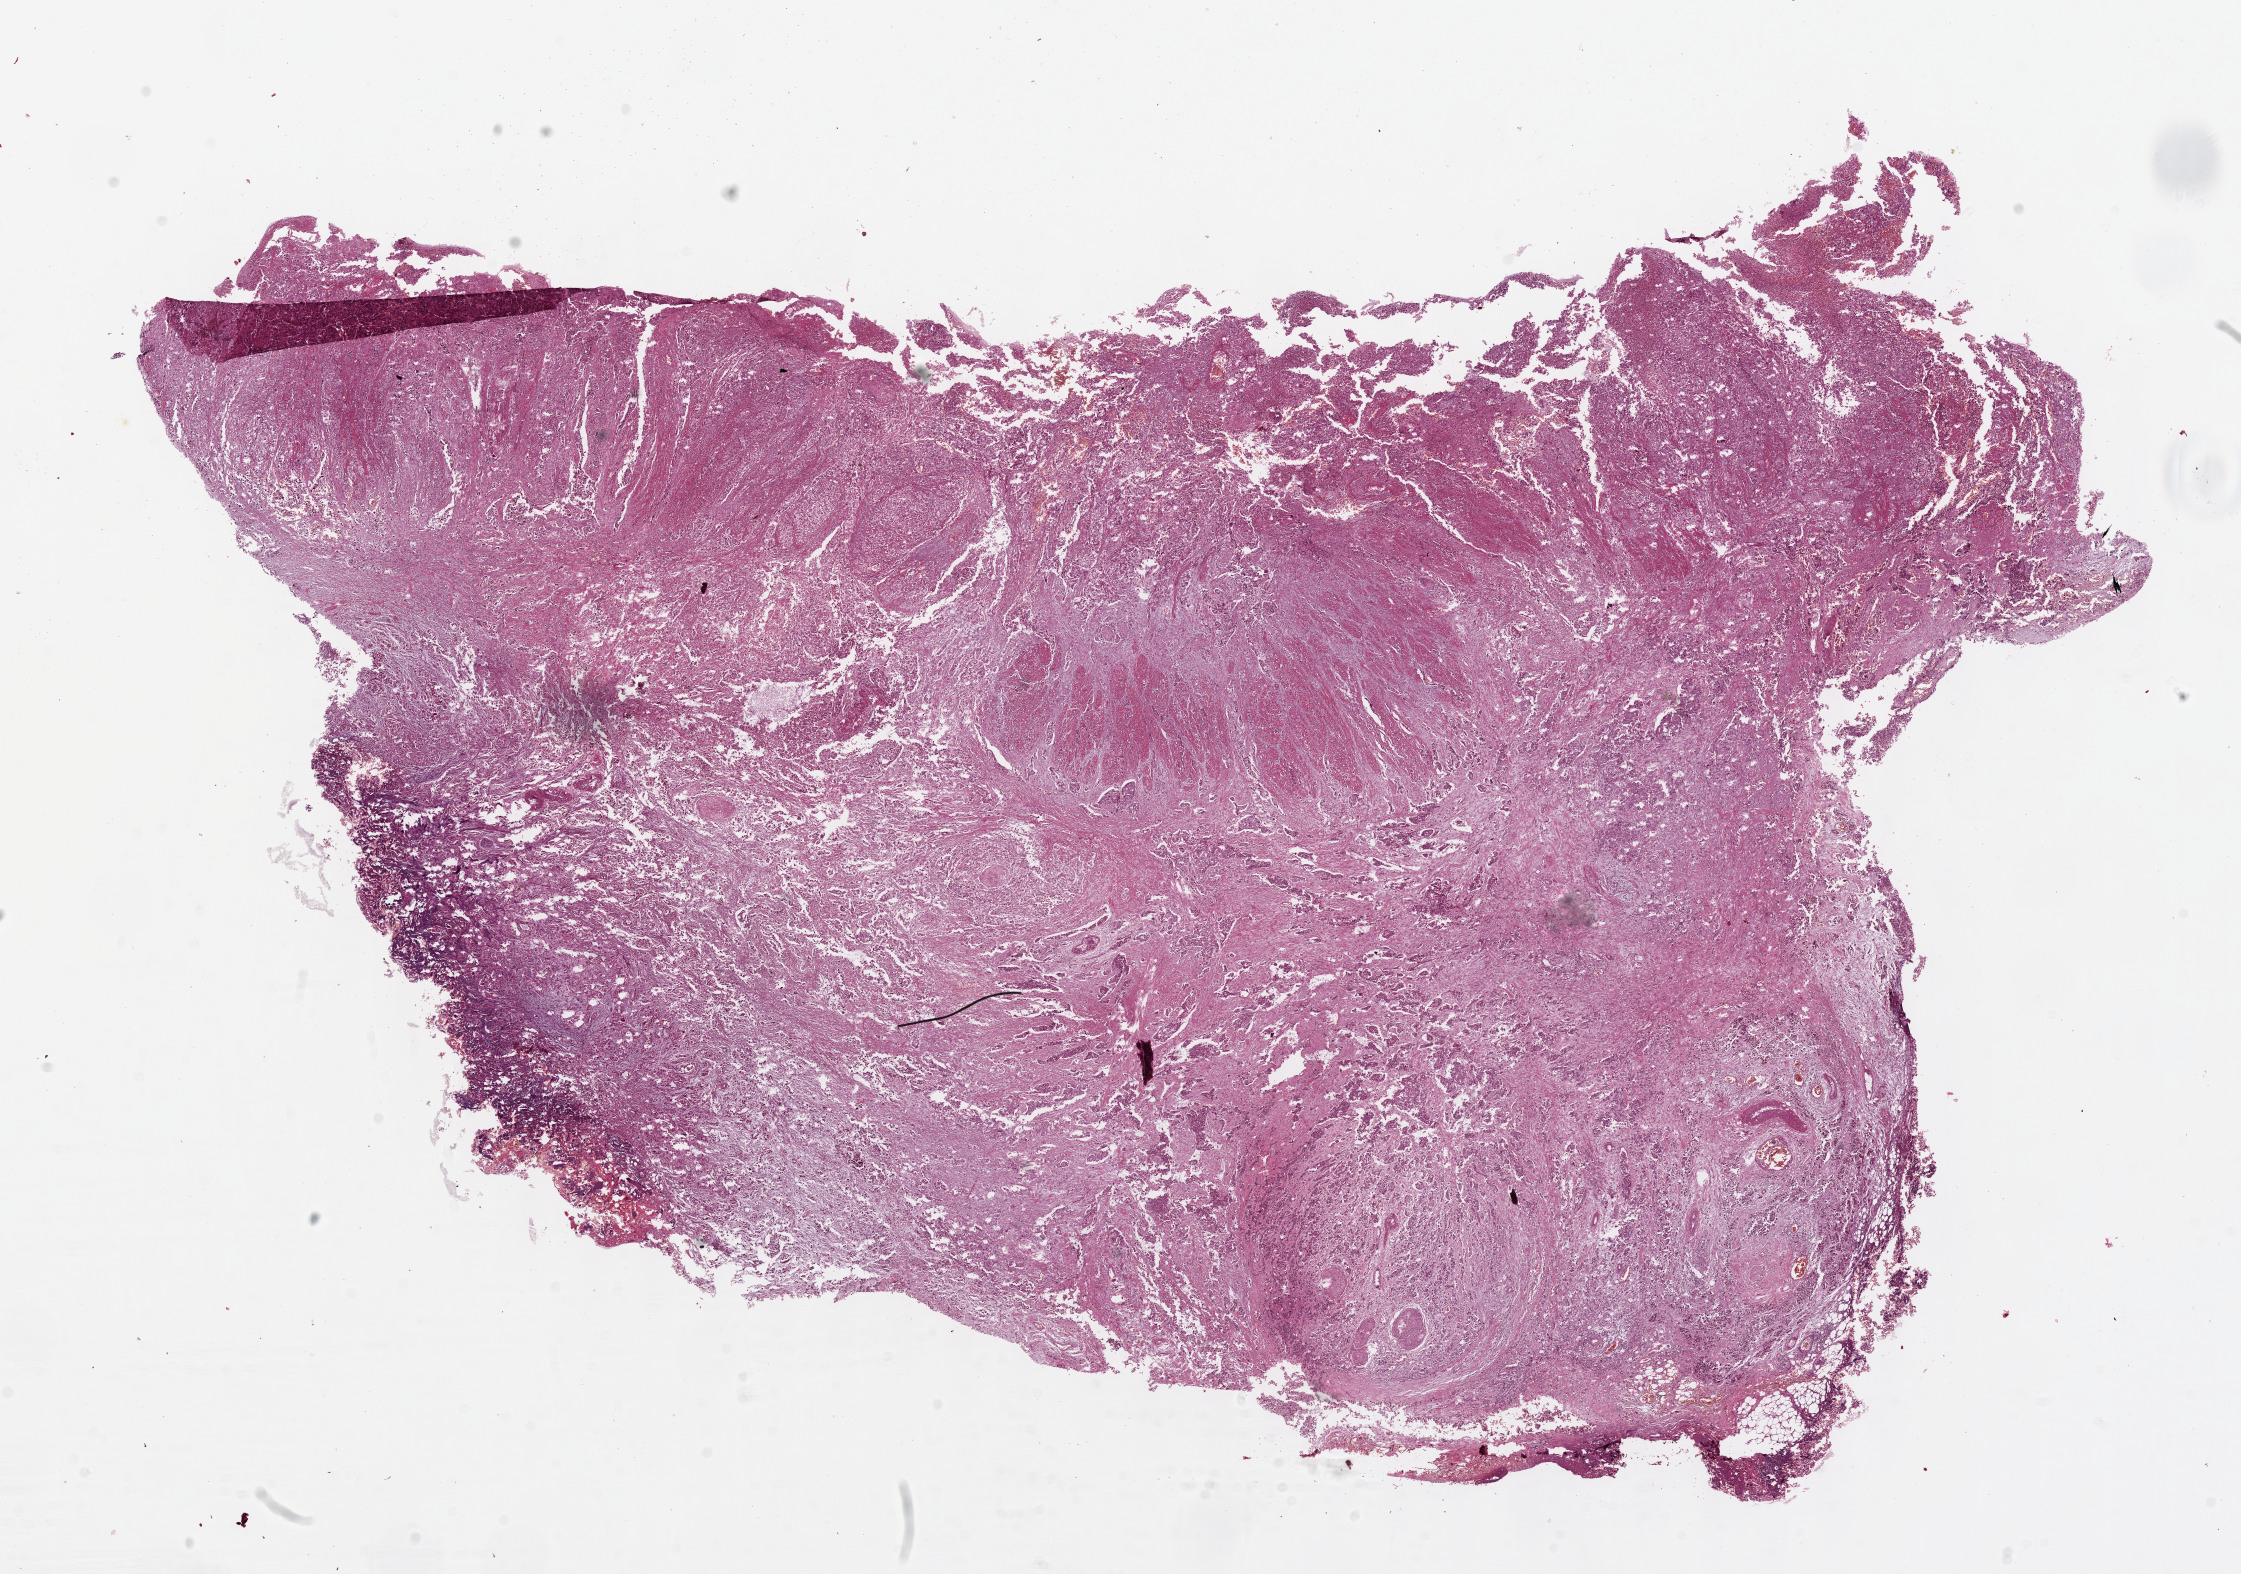
Digitized H&E-stained tissue section (whole slide) — whole scanned area (about 18.1 x 12.7 mm) shown as a low-resolution overview; formalin-fixed paraffin-embedded (FFPE) diagnostic section; sample: primary tumour, esophagus. Male patient; age at initial diagnosis 50 years. Histologic grade: G2 (moderately differentiated).
Pathologic diagnosis: Squamous cell carcinoma, NOS (upper third of esophagus). Lymph nodes positive (case pathology): 1 of 1 examined. AJCC pathologic stage: III (6th edition).